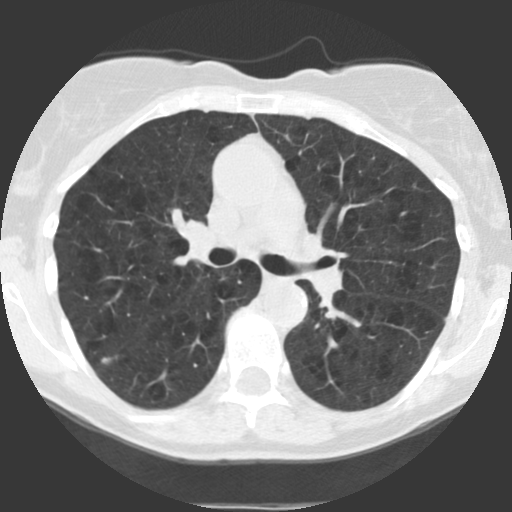
Low-dose screening chest CT, axial slice; baseline annual screen; lung window (W 1500 / L -600 HU); 140 kVp; 512 × 512 image matrix, field of view 290 × 290 mm. Female, age 68 years at enrolment.
Expert reader's lesion annotation, bounding box [x1, y1, x2, y2] px = [90, 340, 127, 375]. The screening reader recorded 2 non-calcified nodules or masses ≥4 mm on this exam; which of them this box marks is not recorded. Official screen result: positive, change unspecified: nodule(s) >= 4 mm or enlarging nodule(s), mass(es), or other non-specific abnormalities suspicious for lung cancer. Participant outcome: lung cancer diagnosed 40 days after this screen — bronchiolo-alveolar adenocarcinoma, NOS, right upper lobe, right middle lobe, right lower lobe, well differentiated (G1), stage IV (AJCC 6th edition).